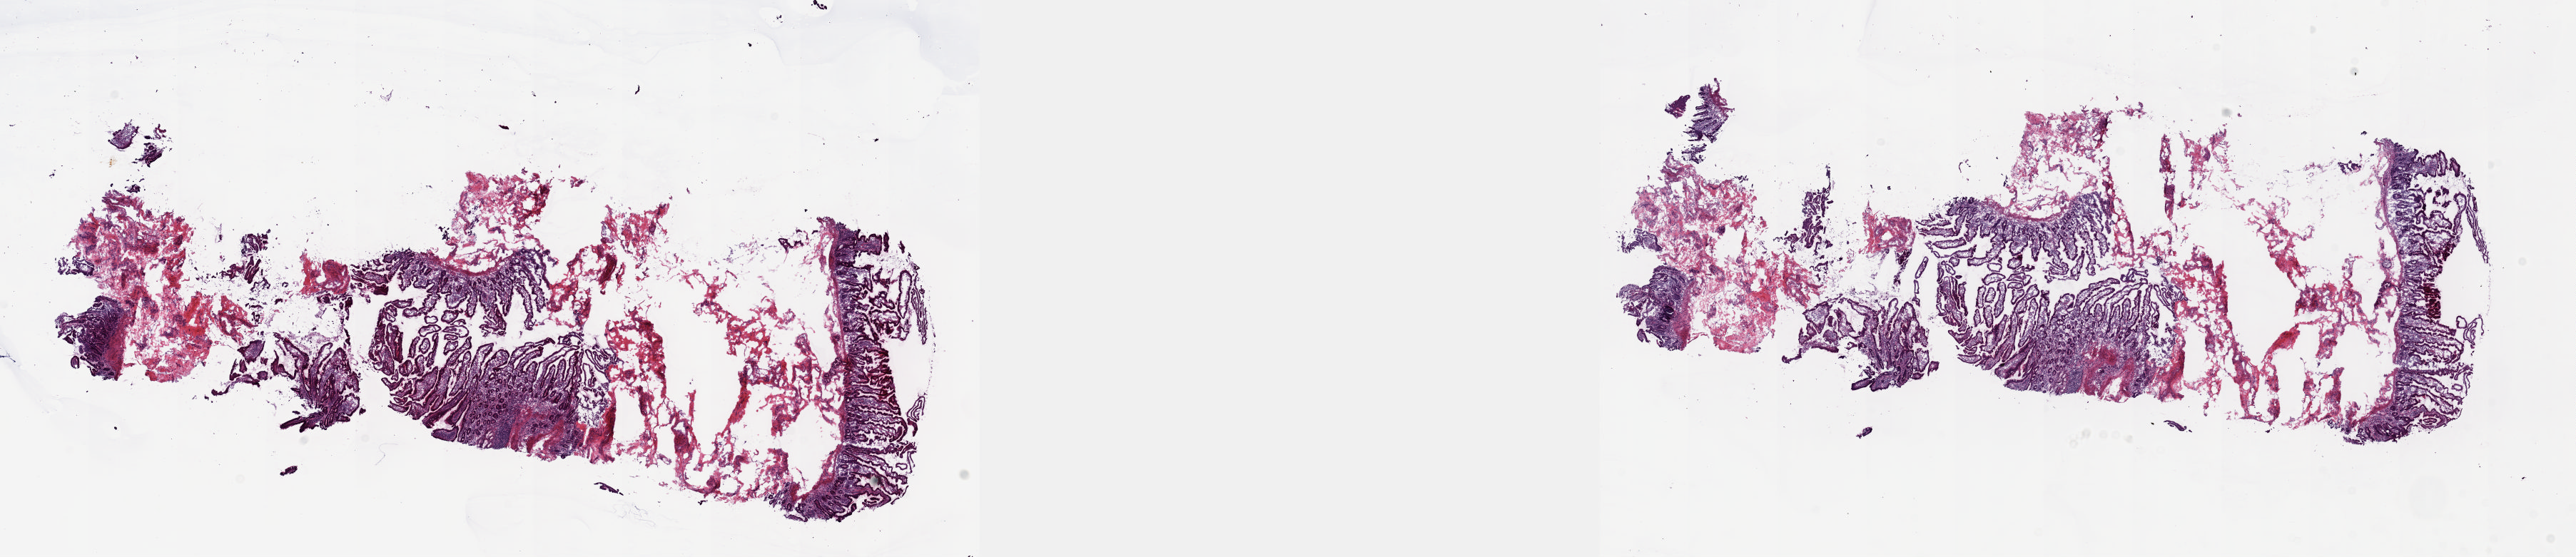
Whole-slide histology image, Hematoxylin and eosin (H&E) stained, a low-resolution overview of the entire scanned area, about 29.1 x 6.3 mm (acquisition: 20x scan). Frozen section from the top of the tissue portion. Pancreas, solid tissue normal (non-tumour tissue) sample. Male patient; age at initial diagnosis 68 years.
This section: solid tissue normal sample (biorepository sample class). Patient diagnosis: Infiltrating duct carcinoma, NOS (head of pancreas).